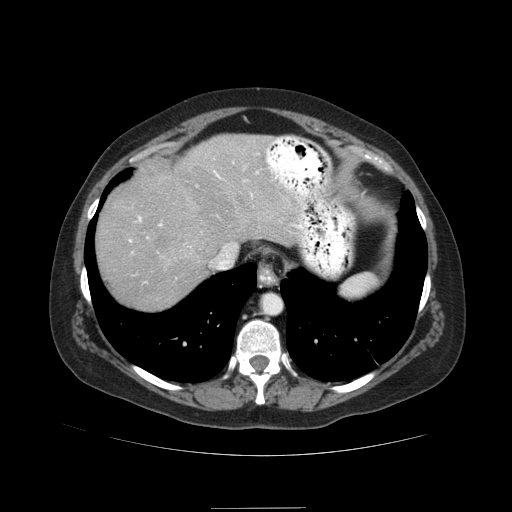
Contrast-enhanced abdominal CT (liver protocol), one axial slice; slice 73 of 89 in the series (ordered by position); soft-tissue window (W 400 / L 40 HU); 2.5 mm slice thickness; 512 × 512 image matrix, field of view 400 × 400 mm. From the clinical record (not read from this slice): diagnosis: hepatocellular carcinoma (patient treated with transarterial chemoembolisation; whether this scan precedes or follows treatment is not stated here); TNM stage (as recorded): Stage-IIIB; Child-Pugh class: A; tumour nodularity: multinodular.
Outlined on this slice (semi-automatically segmented with operator editing):
- liver parenchyma outside the tumour (the mass and vessels are separate outlines, so this box may not span the whole liver): bounding box (x1, y1, x2, y2) in pixels: (96, 134, 302, 310)
- liver vessels: (129, 171, 301, 242)